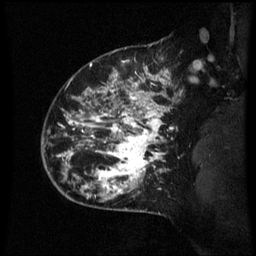
Breast MRI (dynamic contrast-enhanced), one sagittal slice; position 50 of 60 along the scan axis; dynamic contrast-enhanced series, image 2 of 3 at this slice position (ordered by acquisition); 1.5 T; TE 4.2 ms, TR 8.9 ms; 256 × 256 image matrix. Patient: female, 42 years. Case-level facts recorded for this patient, not image findings: setting: breast cancer imaged before/during neoadjuvant chemotherapy; receptor status: HER2-positive.
Structures marked on this image (semi-automatically segmented with operator editing):
- analysis volume of interest (the breast-tissue region the enhancement analysis was run in; not a lesion): bounding box (x1, y1, x2, y2) in pixels: (66, 82, 171, 193)
- tumour enhancement mask (voxels above the 70 % enhancement threshold inside the analysis volume of interest): (66, 82, 169, 193)